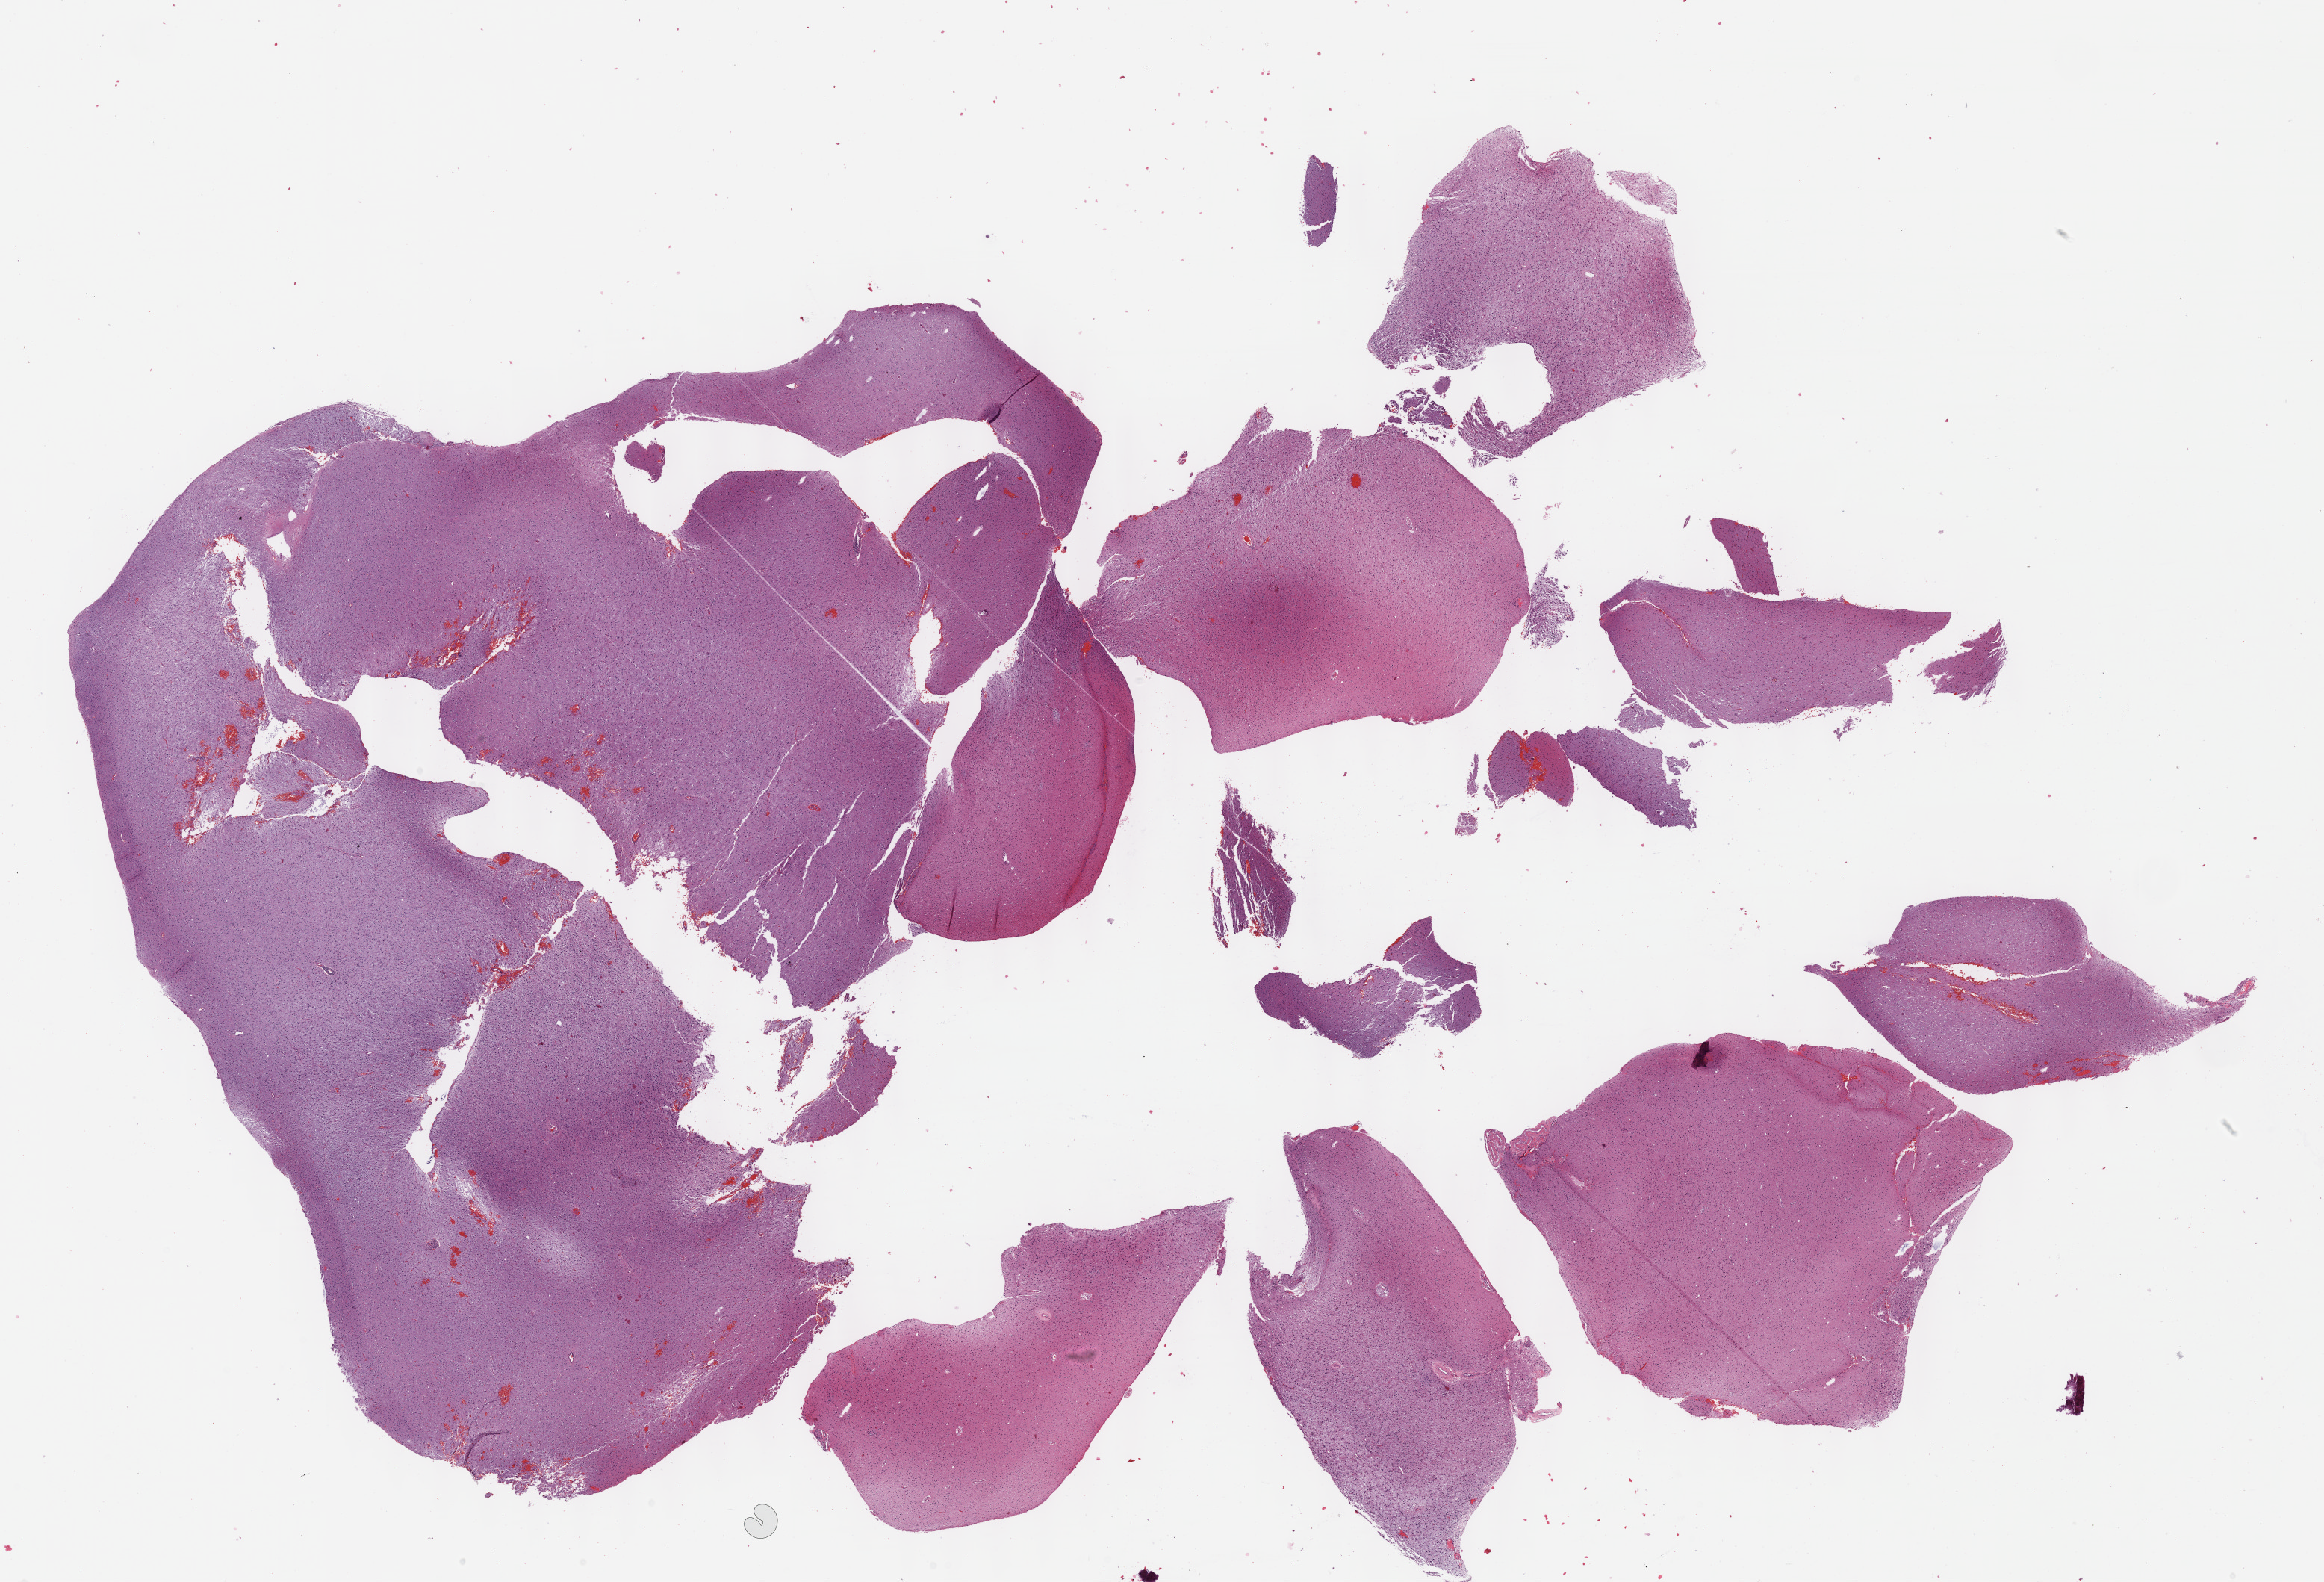
Digitized Hematoxylin and eosin (H&E) stained tissue section (whole slide), low-resolution overview of the scanned area, about 25.1 x 17.1 mm, formalin-fixed paraffin-embedded (FFPE) diagnostic section, brain, primary tumour sample. Male, age 47 years at initial diagnosis. Histologic grade: G2 (moderately differentiated).
• histologic diagnosis: Mixed glioma (cerebrum)